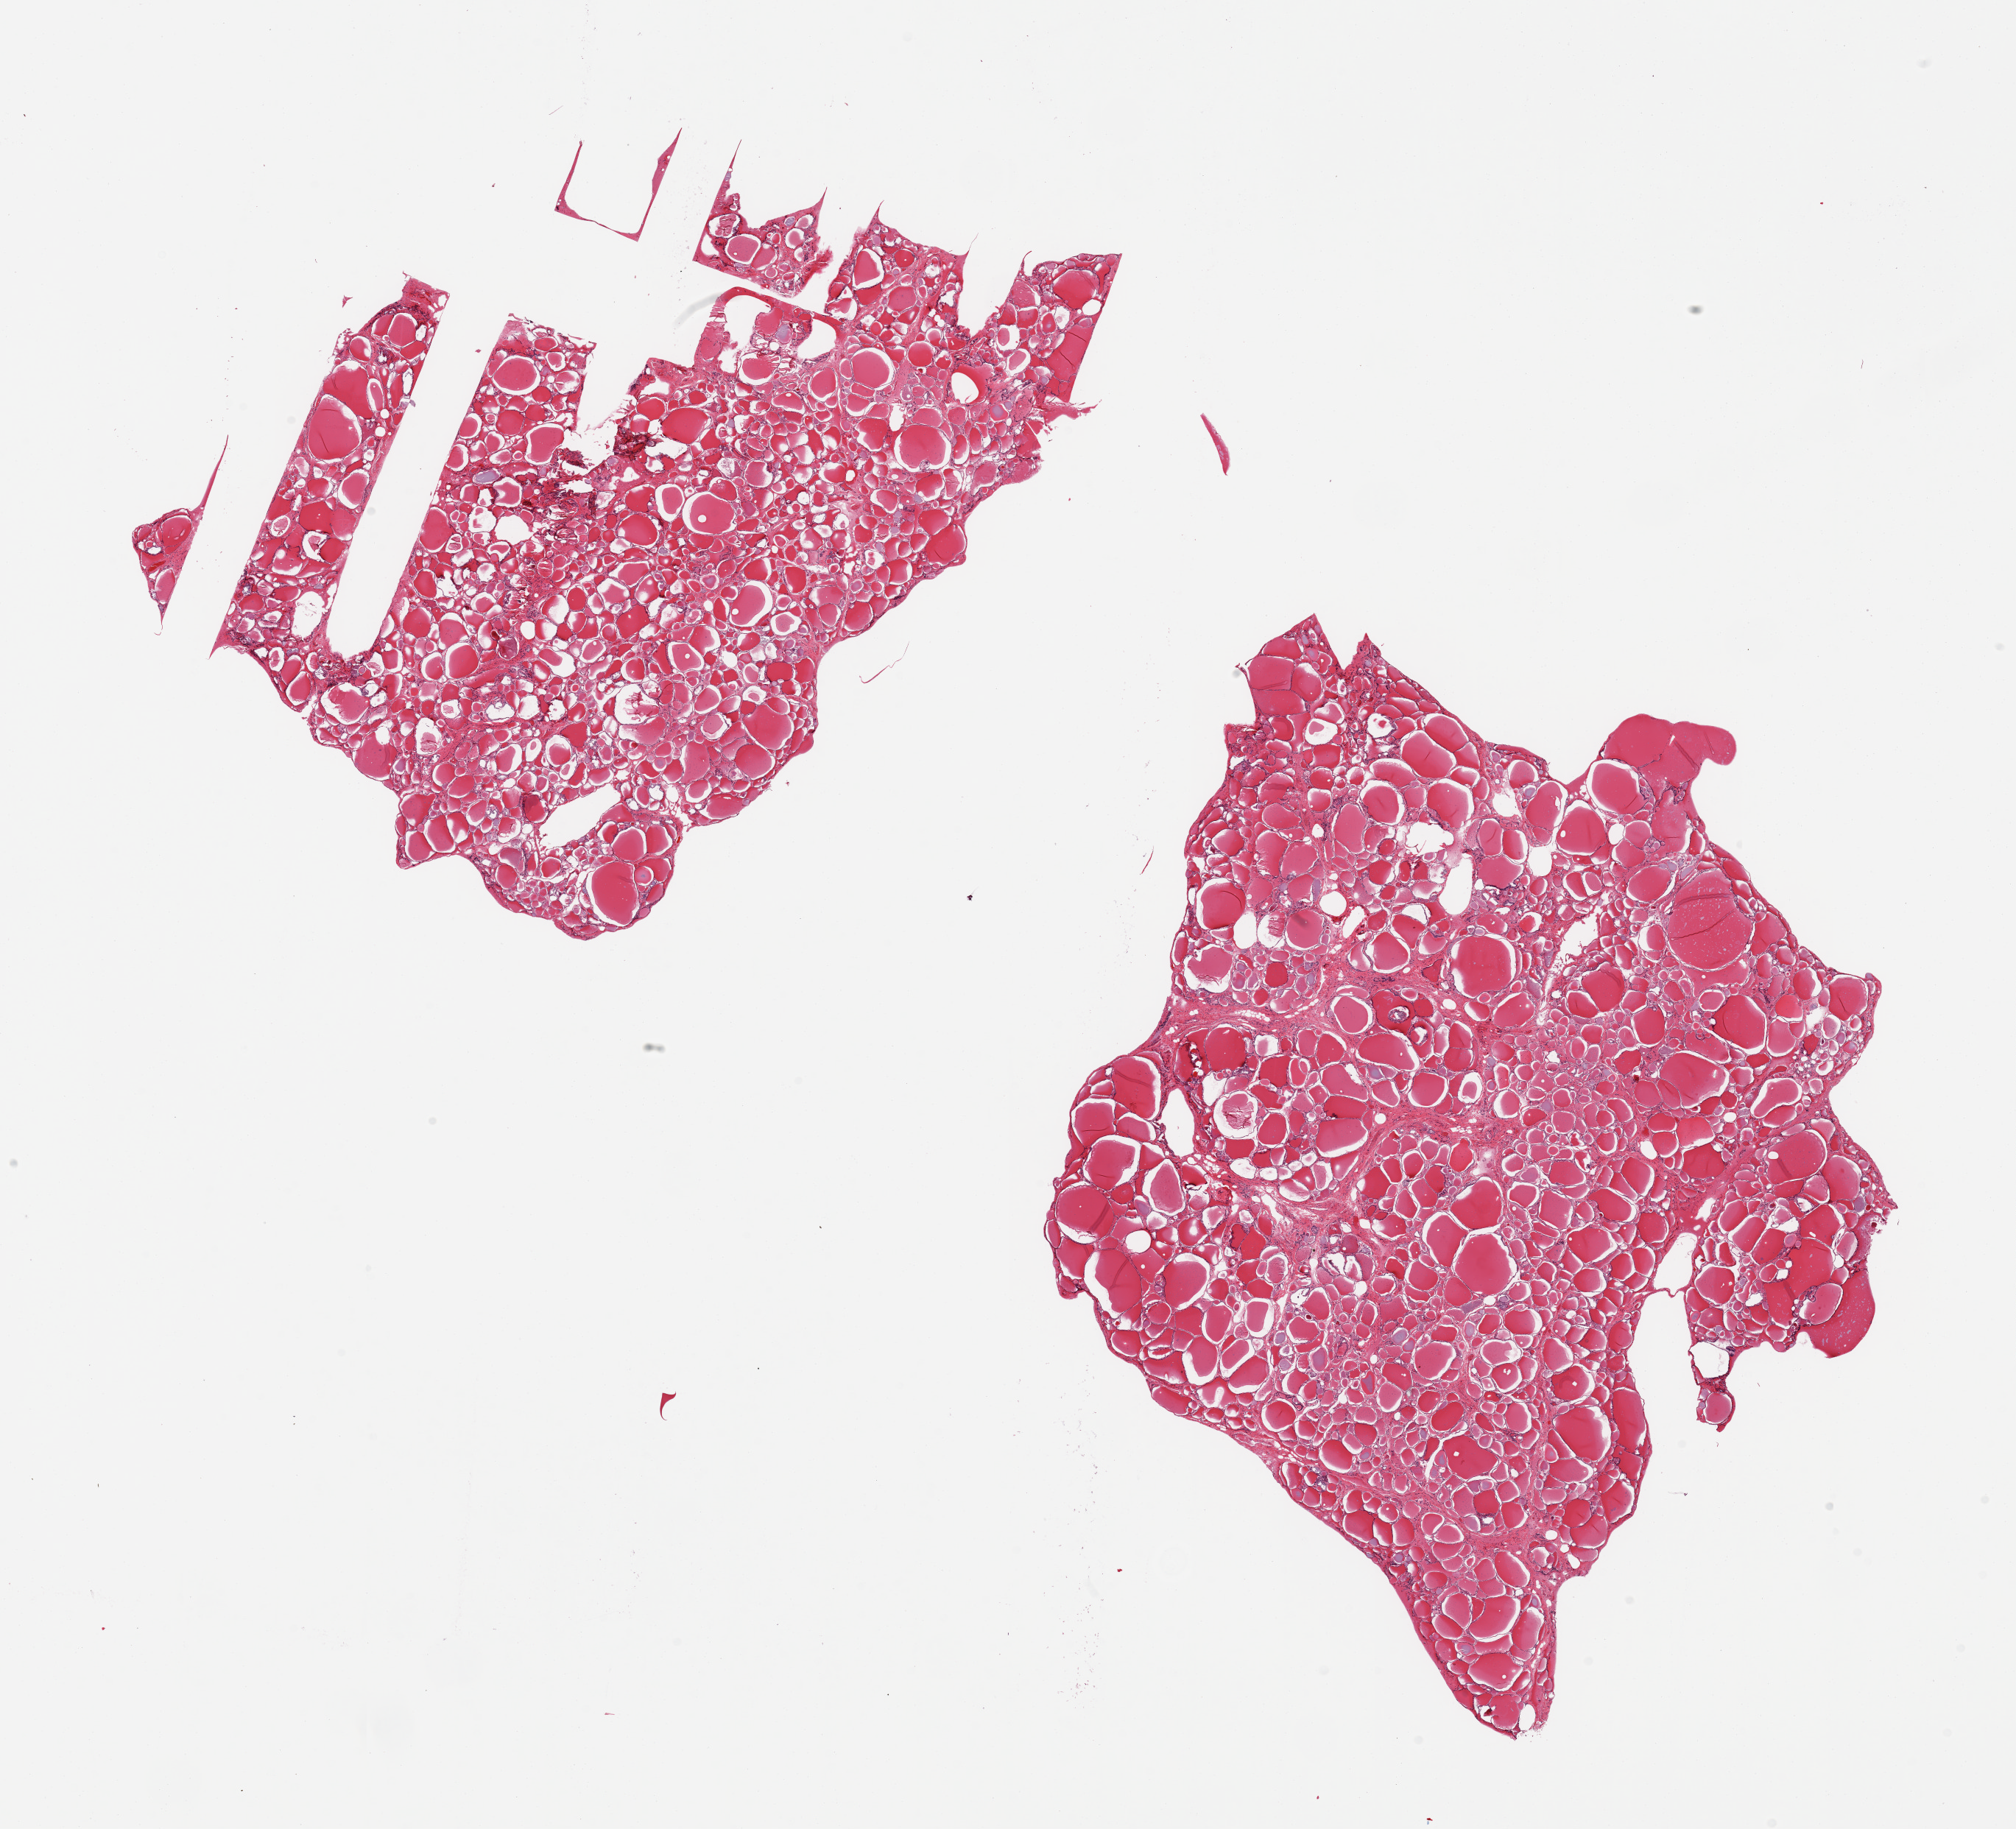
Whole-slide image, hematoxylin and eosin (H&E) stain, shown as a low-resolution overview of the whole scanned area (about 21.7 x 19.6 mm), PAXgene-fixed paraffin-embedded (PFPE) section, target tissue: thyroid, donor tissue sample. Male donor.
Review note (as recorded): 2 pieces, no abnormalities.